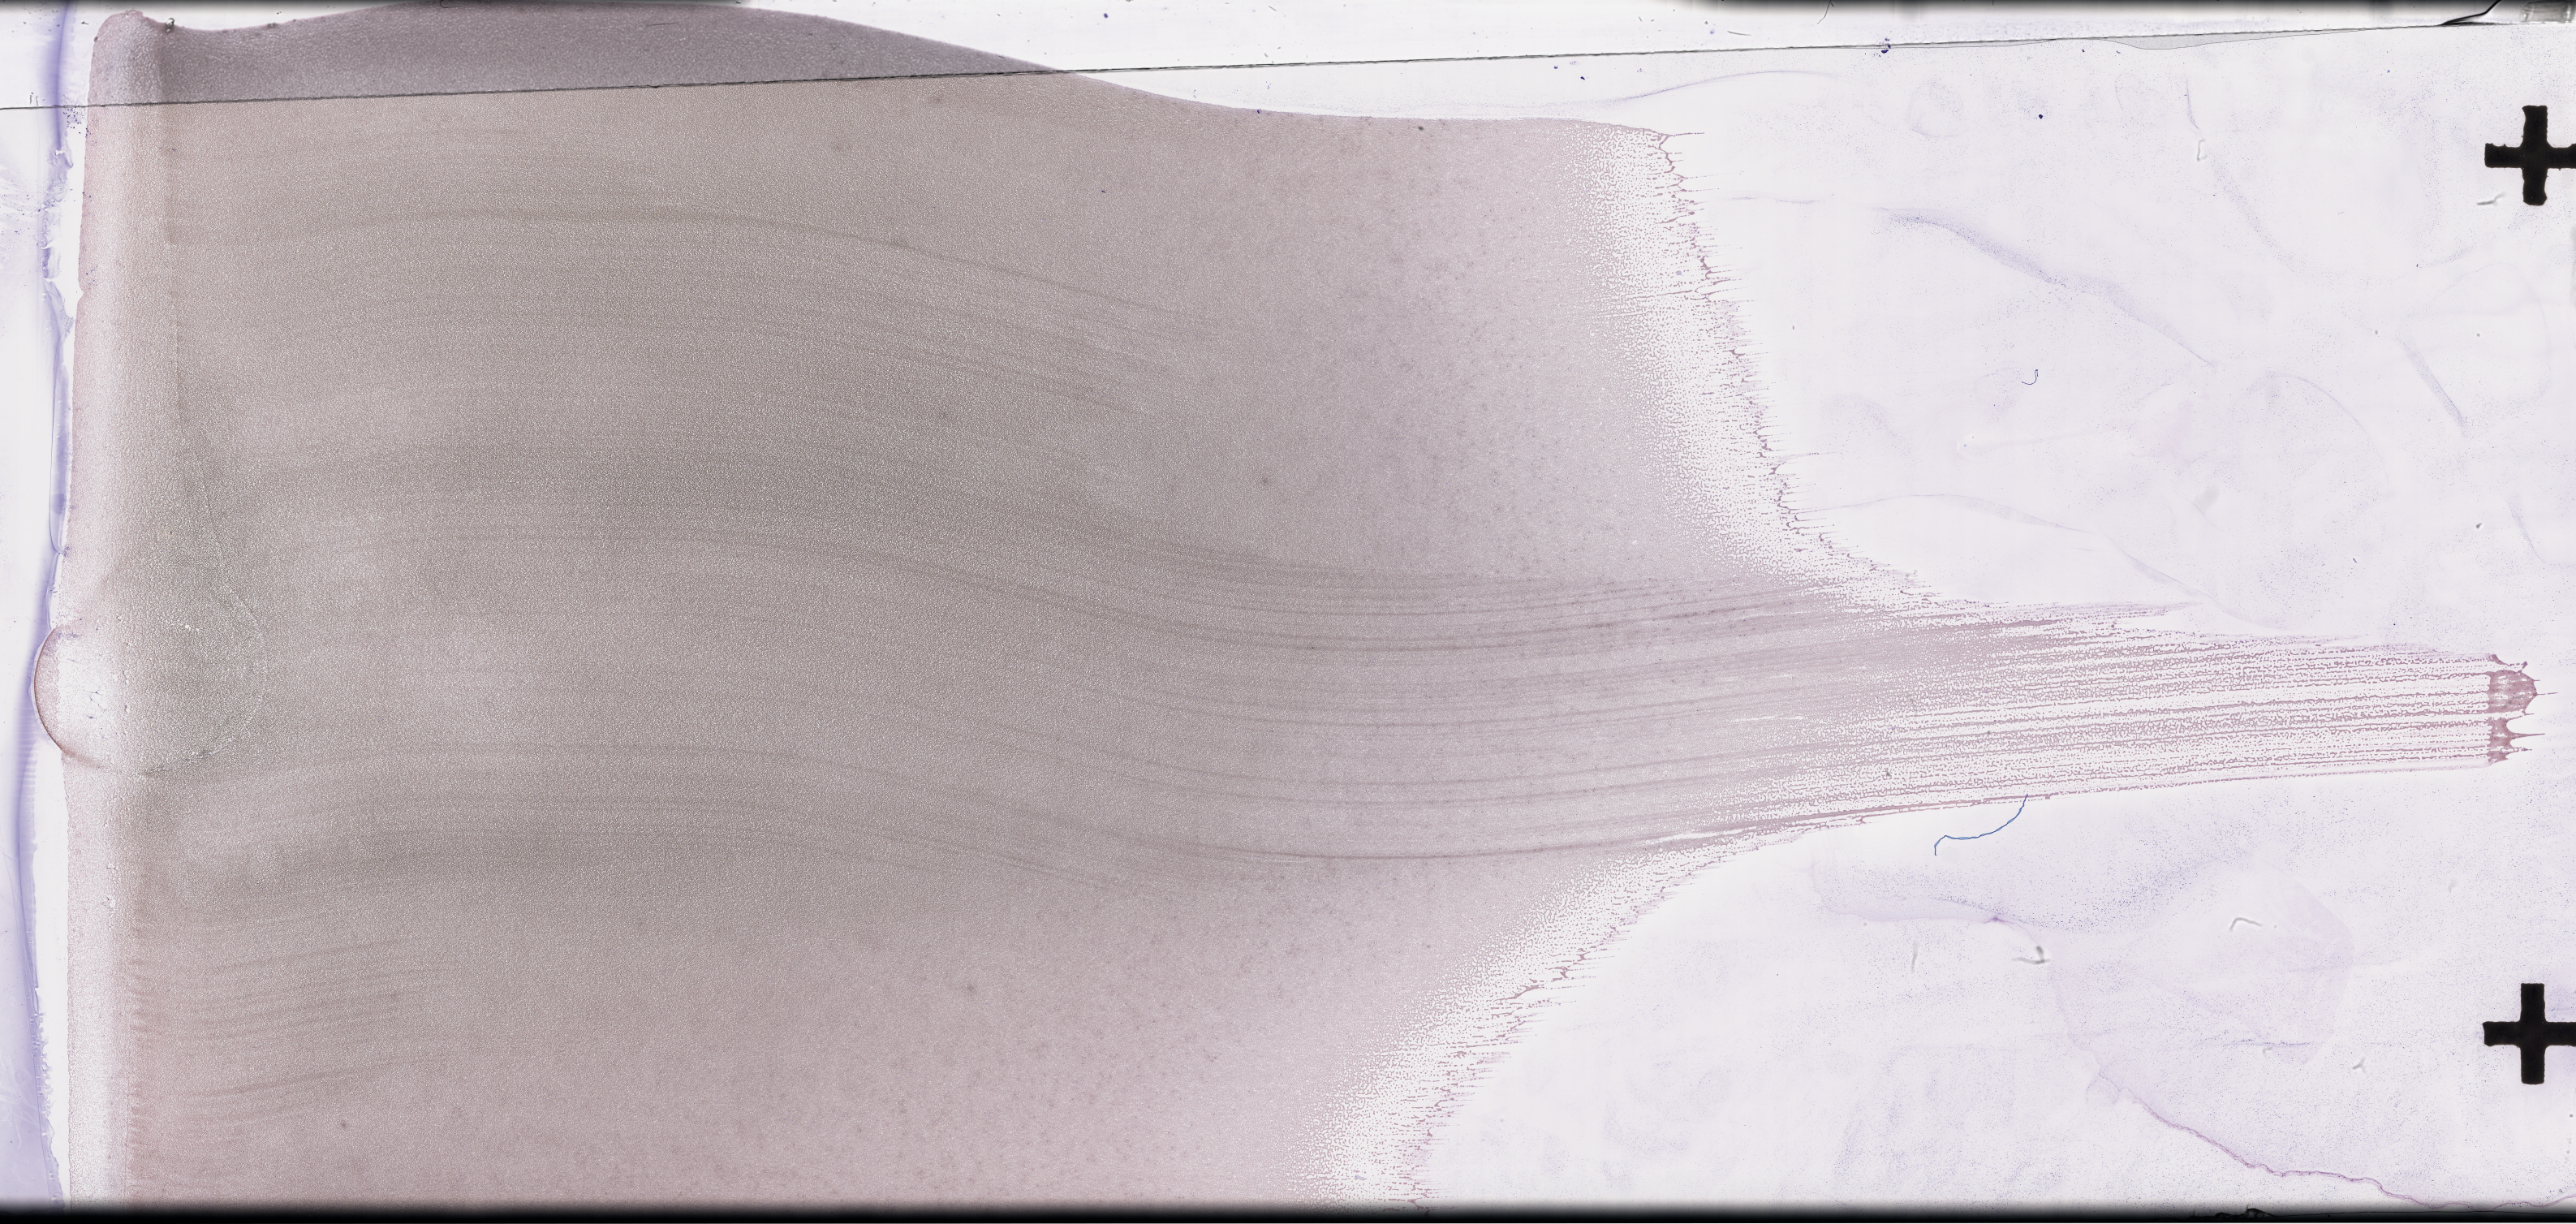
Whole-slide image of a whole blood smear, Wright–Giemsa stain — low-resolution overview of the scanned area, about 51.3 x 24.4 mm, specimen time point: collected on treatment. Patient: male.
Patient diagnosis: Plasma Cell Myeloma.